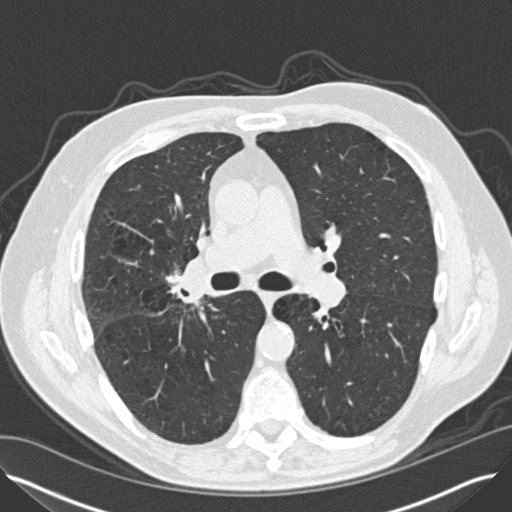
Low-dose screening chest CT, one axial slice; slice 84 of 149 in the series (ordered by position); 120 kVp; lung window (W 1500 / L -600 HU); 512 × 512 image matrix, field of view 370 × 370 mm.
Outlined on this slice (manually delineated by an expert):
- lesion 2 (tumor, hilum of right lung): bounding box <183,259,207,296> (left, top, right, bottom; pixels)